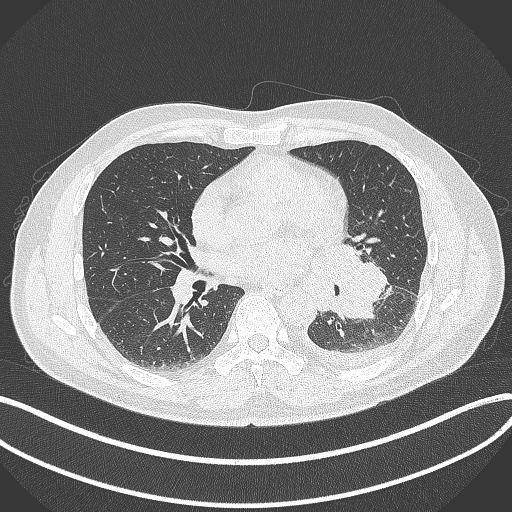
Chest CT, one axial slice; slice 174 of 342 in the series (ordered by position); reconstruction kernel B70f; 120 kVp; lung window (W 1500 / L -600 HU); 1 mm slice thickness; 512 × 512 image matrix. Patient: male, 58 years. Case-level facts recorded for this patient, not image findings: clinical TNM (as recorded): T3 N1 M1b.
Annotated regions visible in this slice (bounding box drawn by a radiologist):
- lung tumour (recorded histology: small cell carcinoma): bounding box [x1, y1, x2, y2] px = [317, 237, 395, 325]